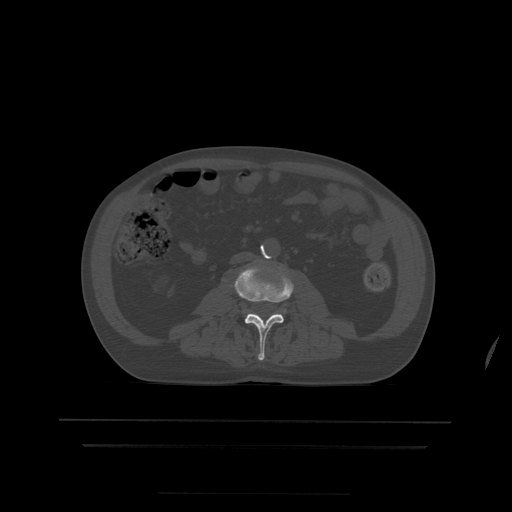
CT including the spine, one axial slice; slice 114 of 522 in the series (ordered by position); bone window (W 1800 / L 400 HU); 1.25 mm slice thickness; 512 × 512 image matrix, field of view 436 × 436 mm. Patient age 68 years. Case-level facts recorded for this patient, not image findings: primary cancer: urothelial.
Outlined on this slice (semi-automatically segmented with operator editing):
- L3 vertebra: box from (x=235, y=266) to (x=294, y=361) px